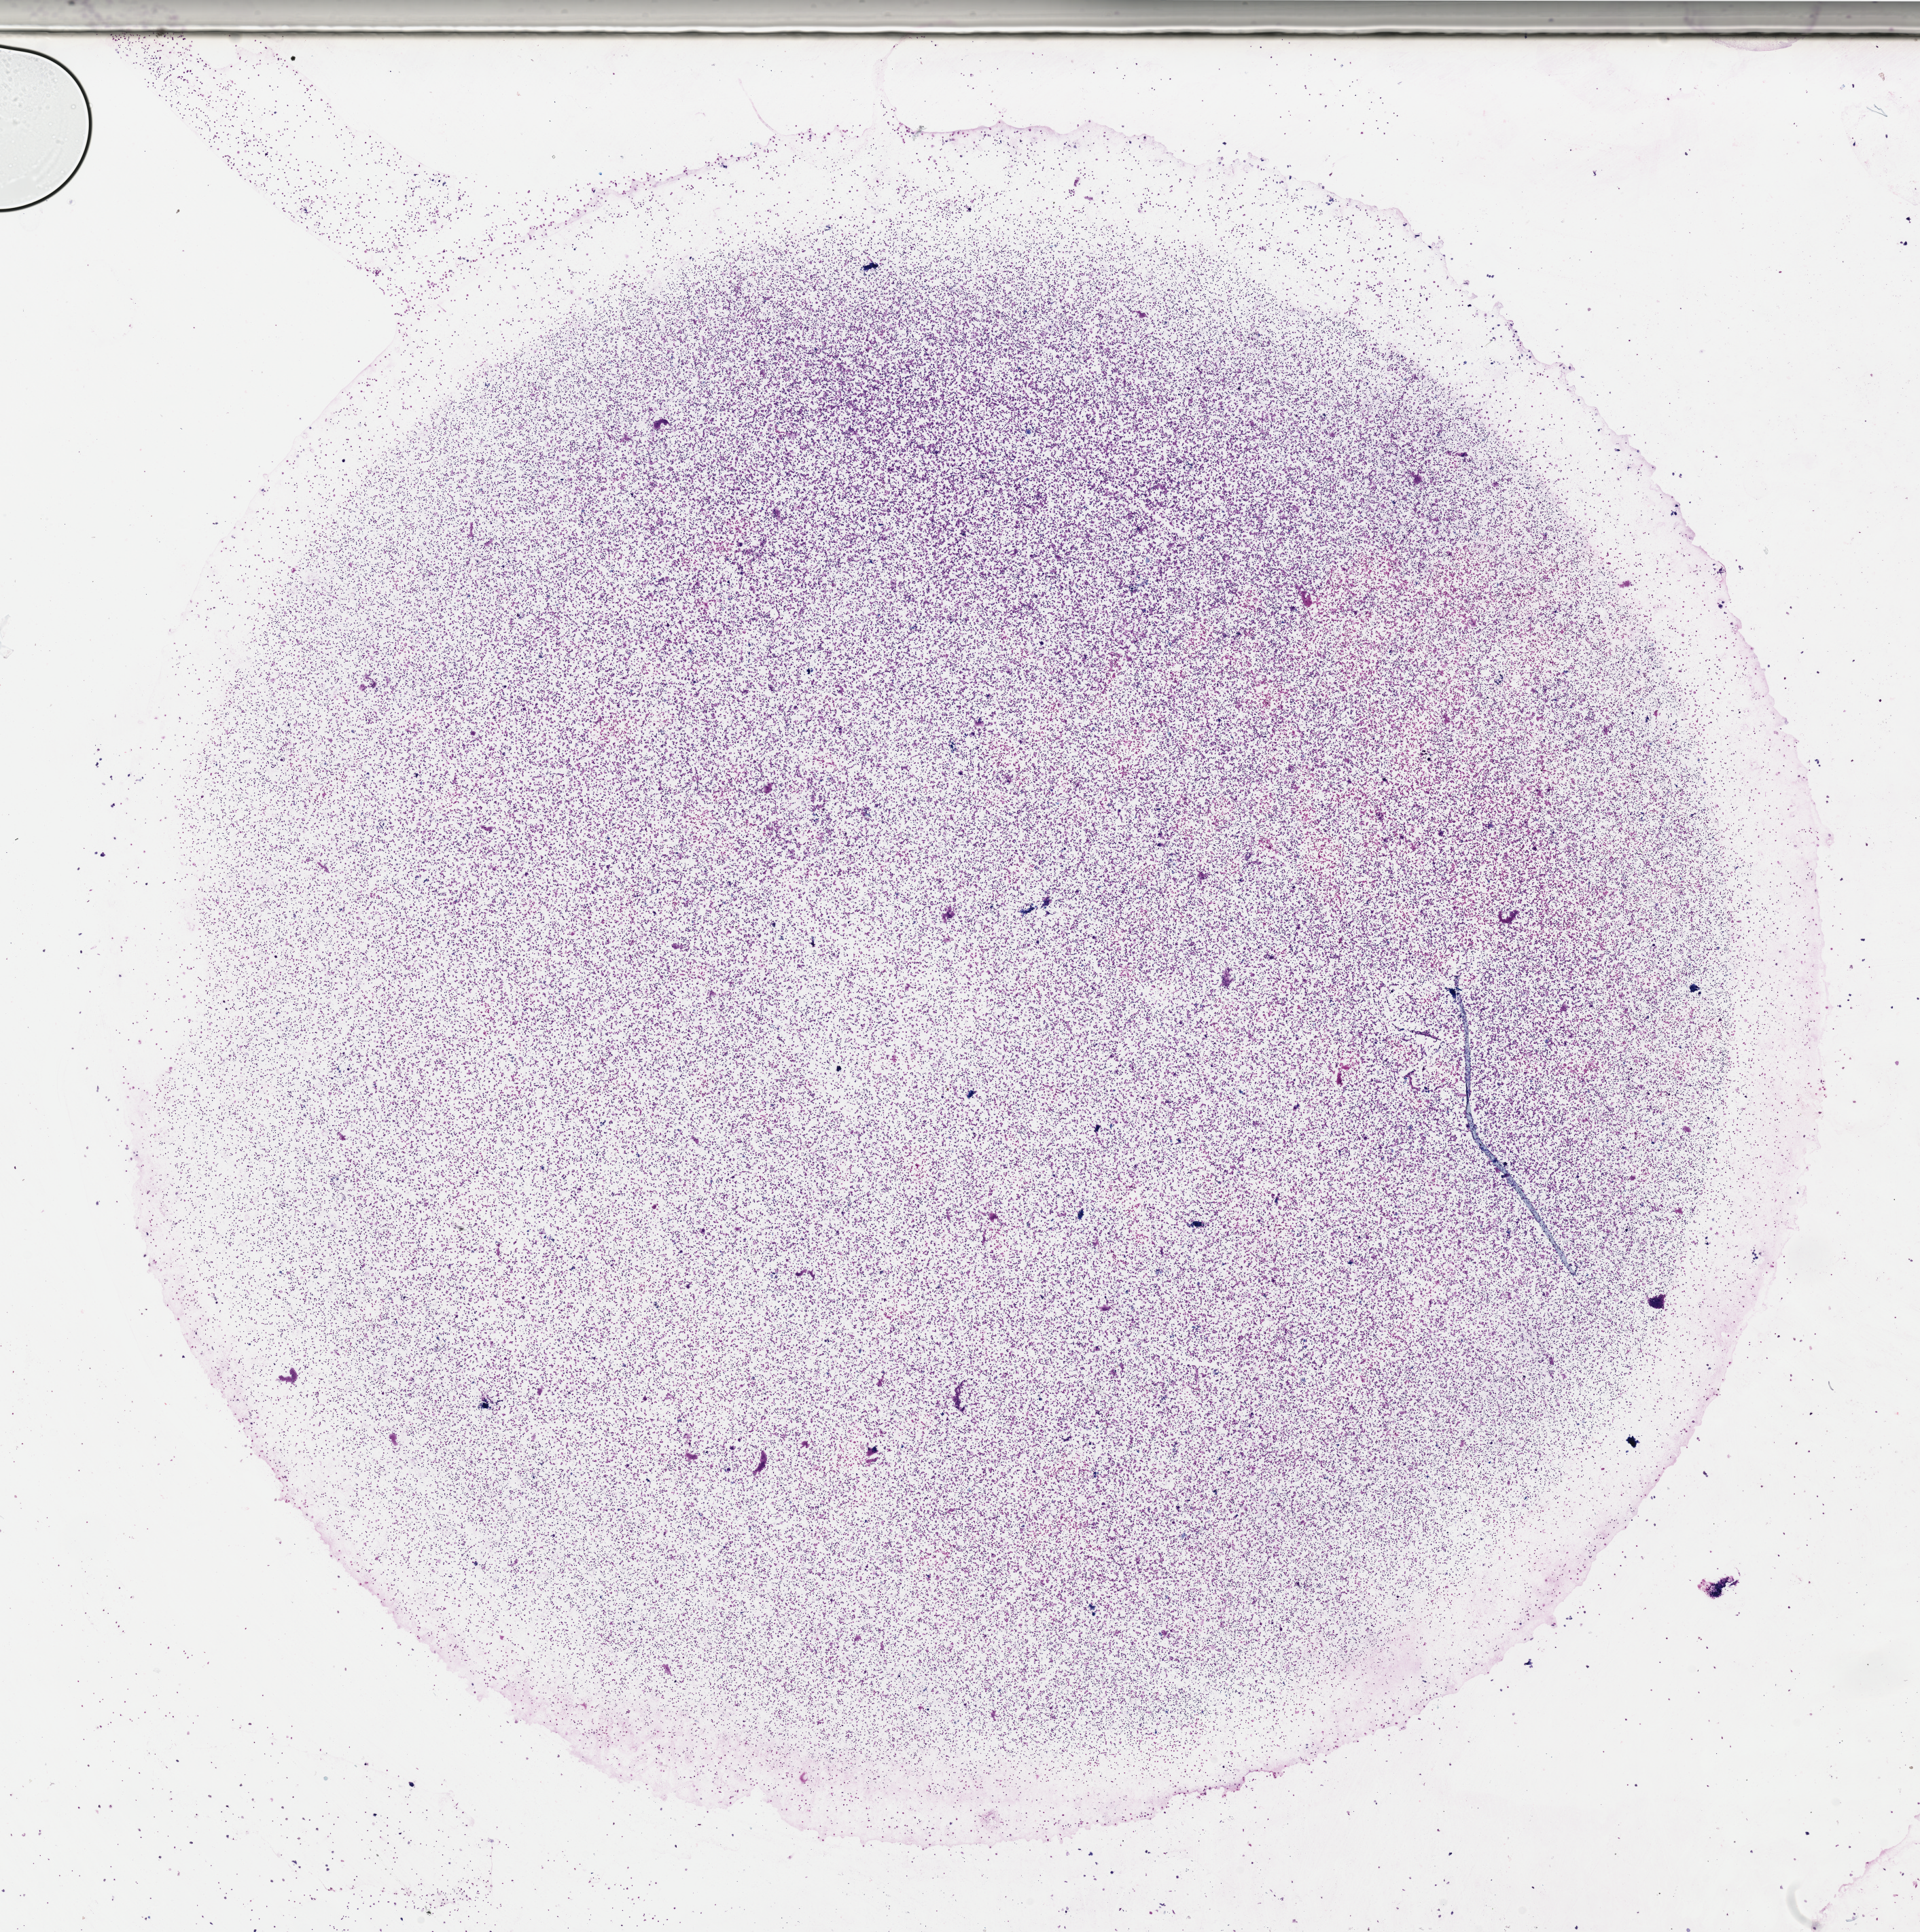
Digitized H&E tissue section (whole slide) — whole scanned area (about 22.3 x 22.4 mm) shown as a low-resolution overview. Bone marrow (leukaemic) sample. 66-year-old female patient.
Diagnosis: Acute Myeloid Leukemia.